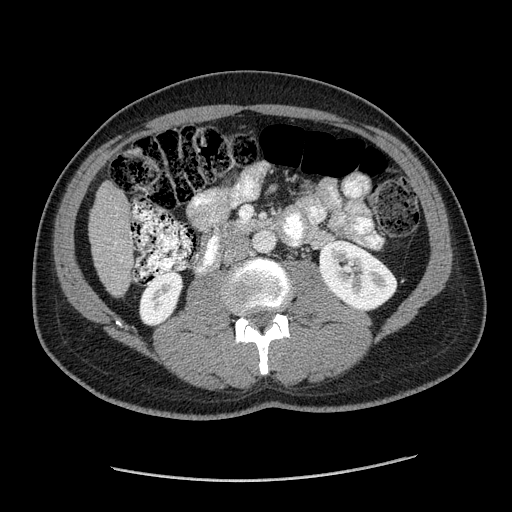
Contrast-enhanced abdominal CT (liver protocol), one axial slice; slice 39 of 182 in the series (ordered by position); reconstruction kernel STANDARD; 120 kVp; soft-tissue window (W 400 / L 40 HU); 2.5 mm slice thickness; 512 × 512 image matrix. Case-level facts recorded for this patient, not image findings: diagnosis: hepatocellular carcinoma (patient treated with transarterial chemoembolisation; whether this scan precedes or follows treatment is not stated here); TNM stage (as recorded): Stage-I.
Structures marked on this image (semi-automatic segmentation, software-assisted and operator-edited):
- liver parenchyma outside the tumour (the mass and vessels are separate outlines, so this box may not span the whole liver): bounding box [x1, y1, x2, y2] px = [88, 180, 133, 294]